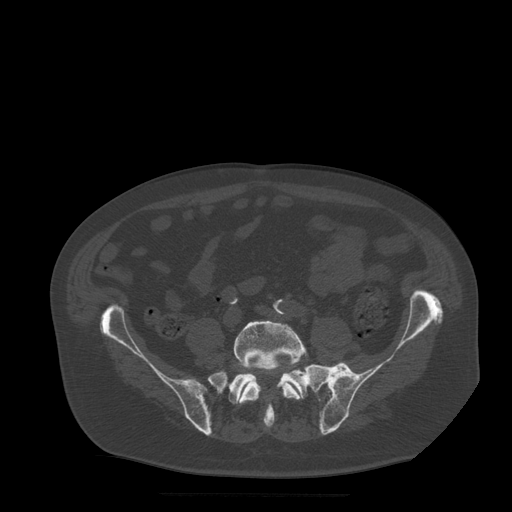
CT including the spine, one axial slice; slice 80 of 522 in the series (ordered by position); bone window (W 1800 / L 400 HU); 1.25 mm slice thickness; 512 × 512 image matrix. Patient age 72 years. From the clinical record (not read from this slice): primary cancer: prostate.
Annotated regions visible in this slice (semi-automatically segmented with operator editing):
- L5 vertebra: bounding box (x1, y1, x2, y2) in pixels: (234, 321, 306, 421)